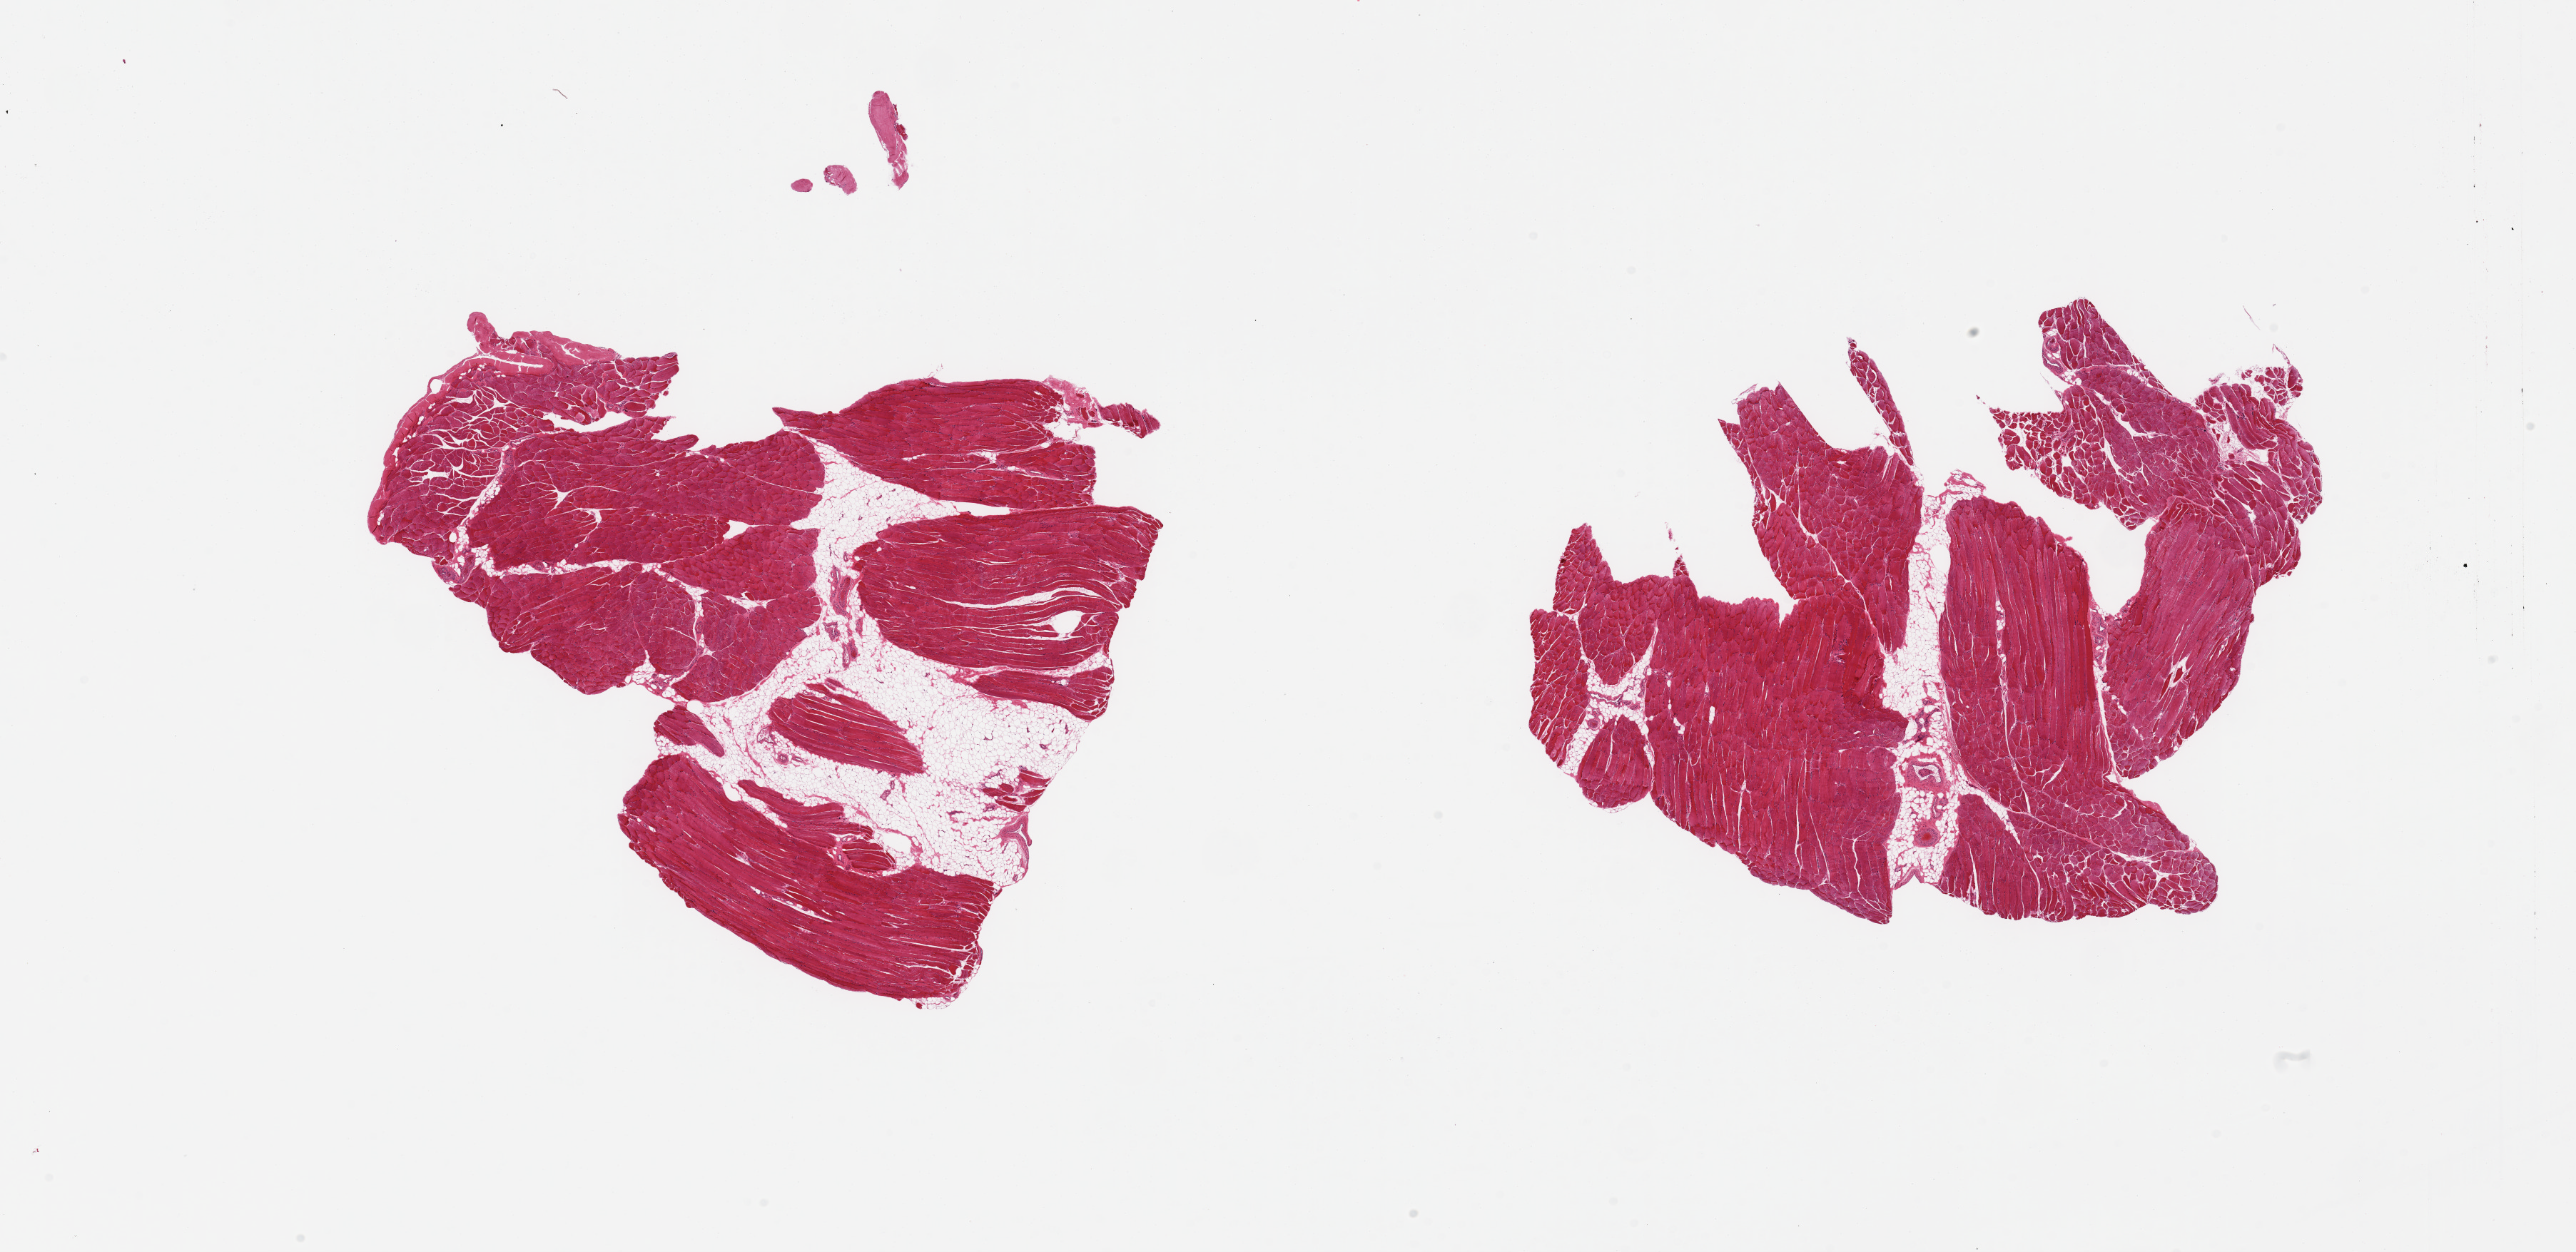
H&E whole-slide image, brightfield — a low-resolution overview of the entire scanned area, about 28.5 x 13.9 mm (slide scanned at 20x), PAXgene-fixed, paraffin-embedded tissue, target tissue: skeletal muscle, donor tissue sample.
• reviewer comment on this tissue sample: 2 pieces; ~15 and 30% internal fat